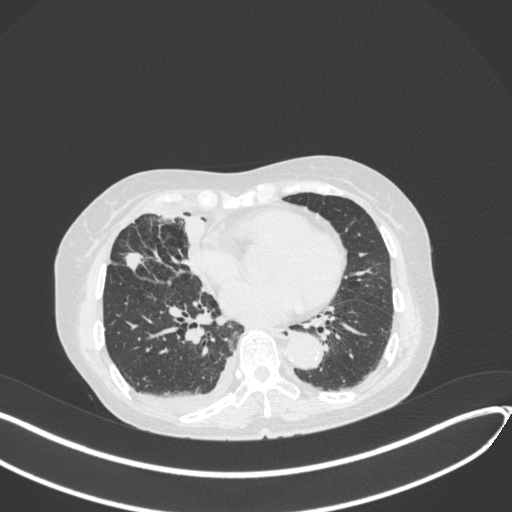
Chest CT, one axial slice. Position 162 of 418 along the scan axis. 120 kVp. Lung window (W 1500 / L -600 HU). 1 mm slice thickness. 512 × 512 image matrix, field of view 400 × 400 mm. Female patient, age 75 years. From the clinical record (not read from this slice): clinical TNM (as recorded): T2a N3 M0.
Outlined on this slice (rectangle marked by the reading radiologist):
- lung tumour (recorded histology: adenocarcinoma): bounding box [x1, y1, x2, y2] px = [123, 247, 147, 271]